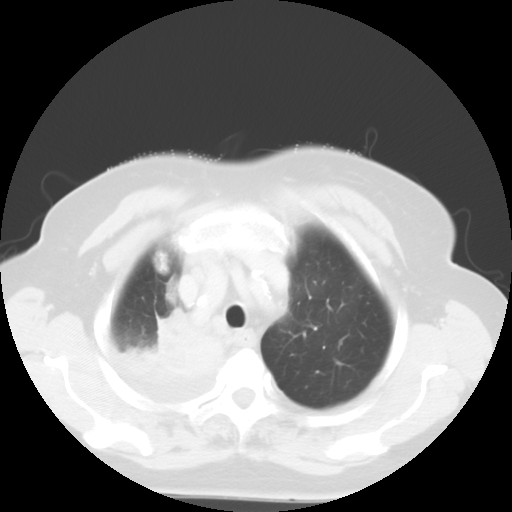
Chest CT, one axial slice; position 44 of 52 along the scan axis; 120 kVp; lung window (W 1500 / L -600 HU); 5 mm slice thickness; 512 × 512 image matrix, field of view 333 × 333 mm. Female patient, age 81 years. From the clinical record (not read from this slice): clinical TNM (as recorded): T4 N3 M1b.
Outlined on this slice (rectangle marked by the reading radiologist):
- lung tumour (recorded histology: adenocarcinoma): box from (x=117, y=305) to (x=227, y=387) px